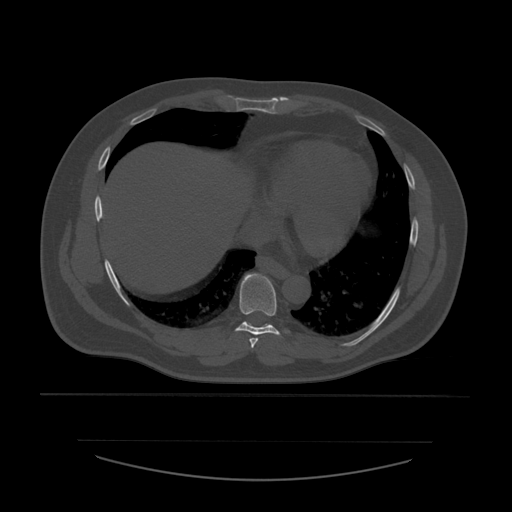
CT including the spine, one axial slice; slice 337 of 532 in the series (ordered by position); 120 kVp; bone window (W 1800 / L 400 HU); 1.25 mm slice thickness; 512 × 512 image matrix, field of view 441 × 441 mm. Patient age 44 years. Case-level facts recorded for this patient, not image findings: primary cancer: soft tissue sarcoma.
Structures marked on this image (semi-automatic segmentation, software-assisted and operator-edited):
- T7 vertebra: bounding box (x1, y1, x2, y2) in pixels: (249, 338, 259, 349)
- T8 vertebra: (235, 274, 281, 336)